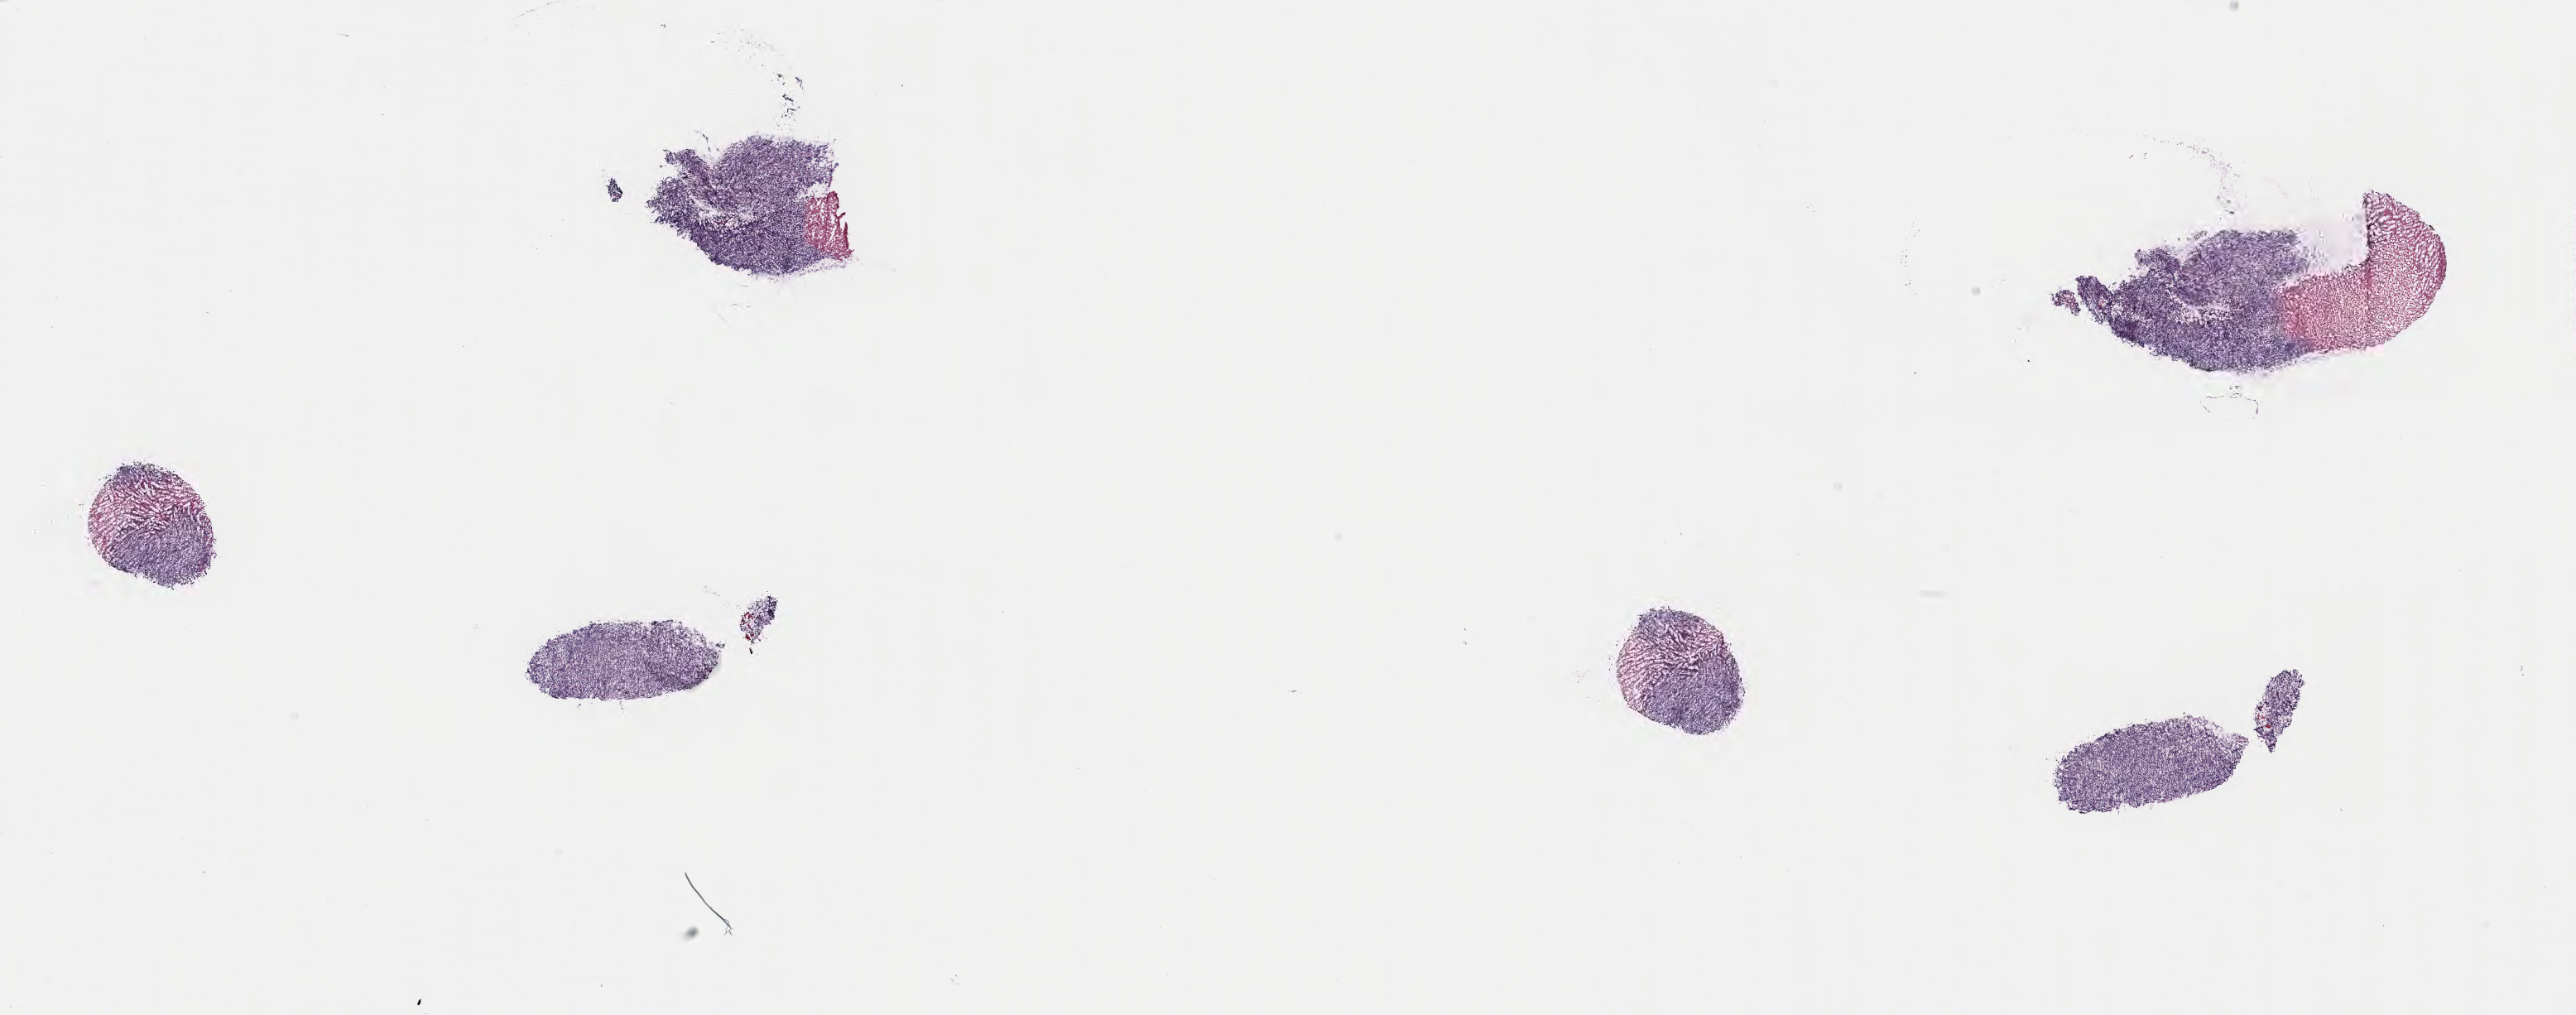
Whole-slide image, H&E stain — low-resolution overview of the scanned area, about 25.2 x 9.9 mm; frozen section; primary tumor; anatomic site: kidney. Male patient; age at initial diagnosis 9 years. Composition of this section per pathologist review: tumor cells 85%, tumor nuclei 90%.
Diagnosis: Burkitt lymphoma, NOS.